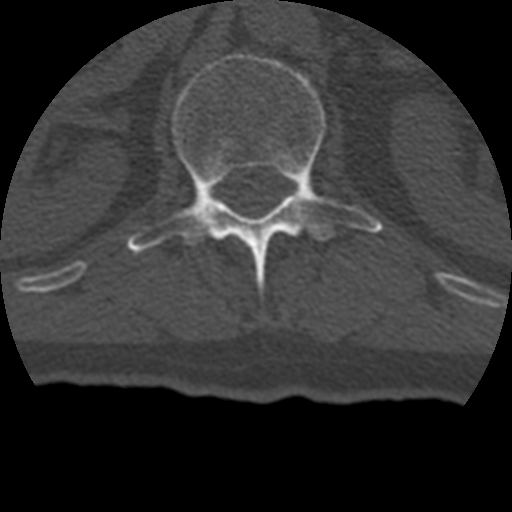
CT including the spine, one axial slice; position 144 of 399 along the scan axis; bone window (W 1800 / L 400 HU); 512 × 512 image matrix, field of view 160 × 160 mm. Patient age 69 years. From the clinical record (not read from this slice): primary cancer: prostate.
Annotated regions visible in this slice (semi-automatically segmented with operator editing):
- L1 vertebra: bounding box [x1, y1, x2, y2] px = [127, 53, 384, 287]